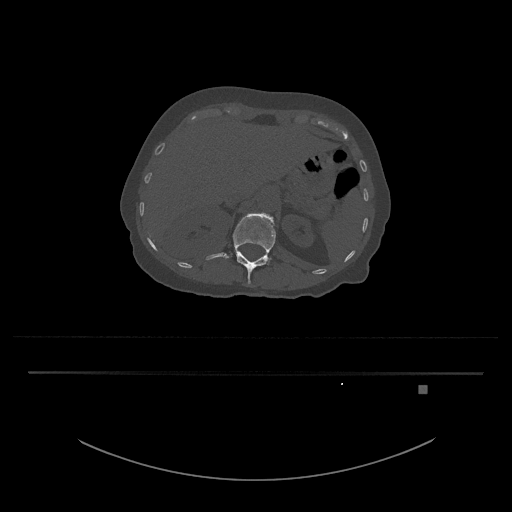
CT including the spine, one axial slice. Slice 550 of 797 in the series (ordered by position). Reconstruction kernel Br40s/3. 120 kVp. Bone window (W 1800 / L 400 HU). 0.5 mm slice thickness. 512 × 512 image matrix, field of view 500 × 500 mm. Female patient, age 57 years. Case-level facts recorded for this patient, not image findings: primary cancer: cervical.
Annotated regions visible in this slice (semi-automatic segmentation, software-assisted and operator-edited):
- L1 vertebra: bounding box <206,212,276,284> (left, top, right, bottom; pixels)